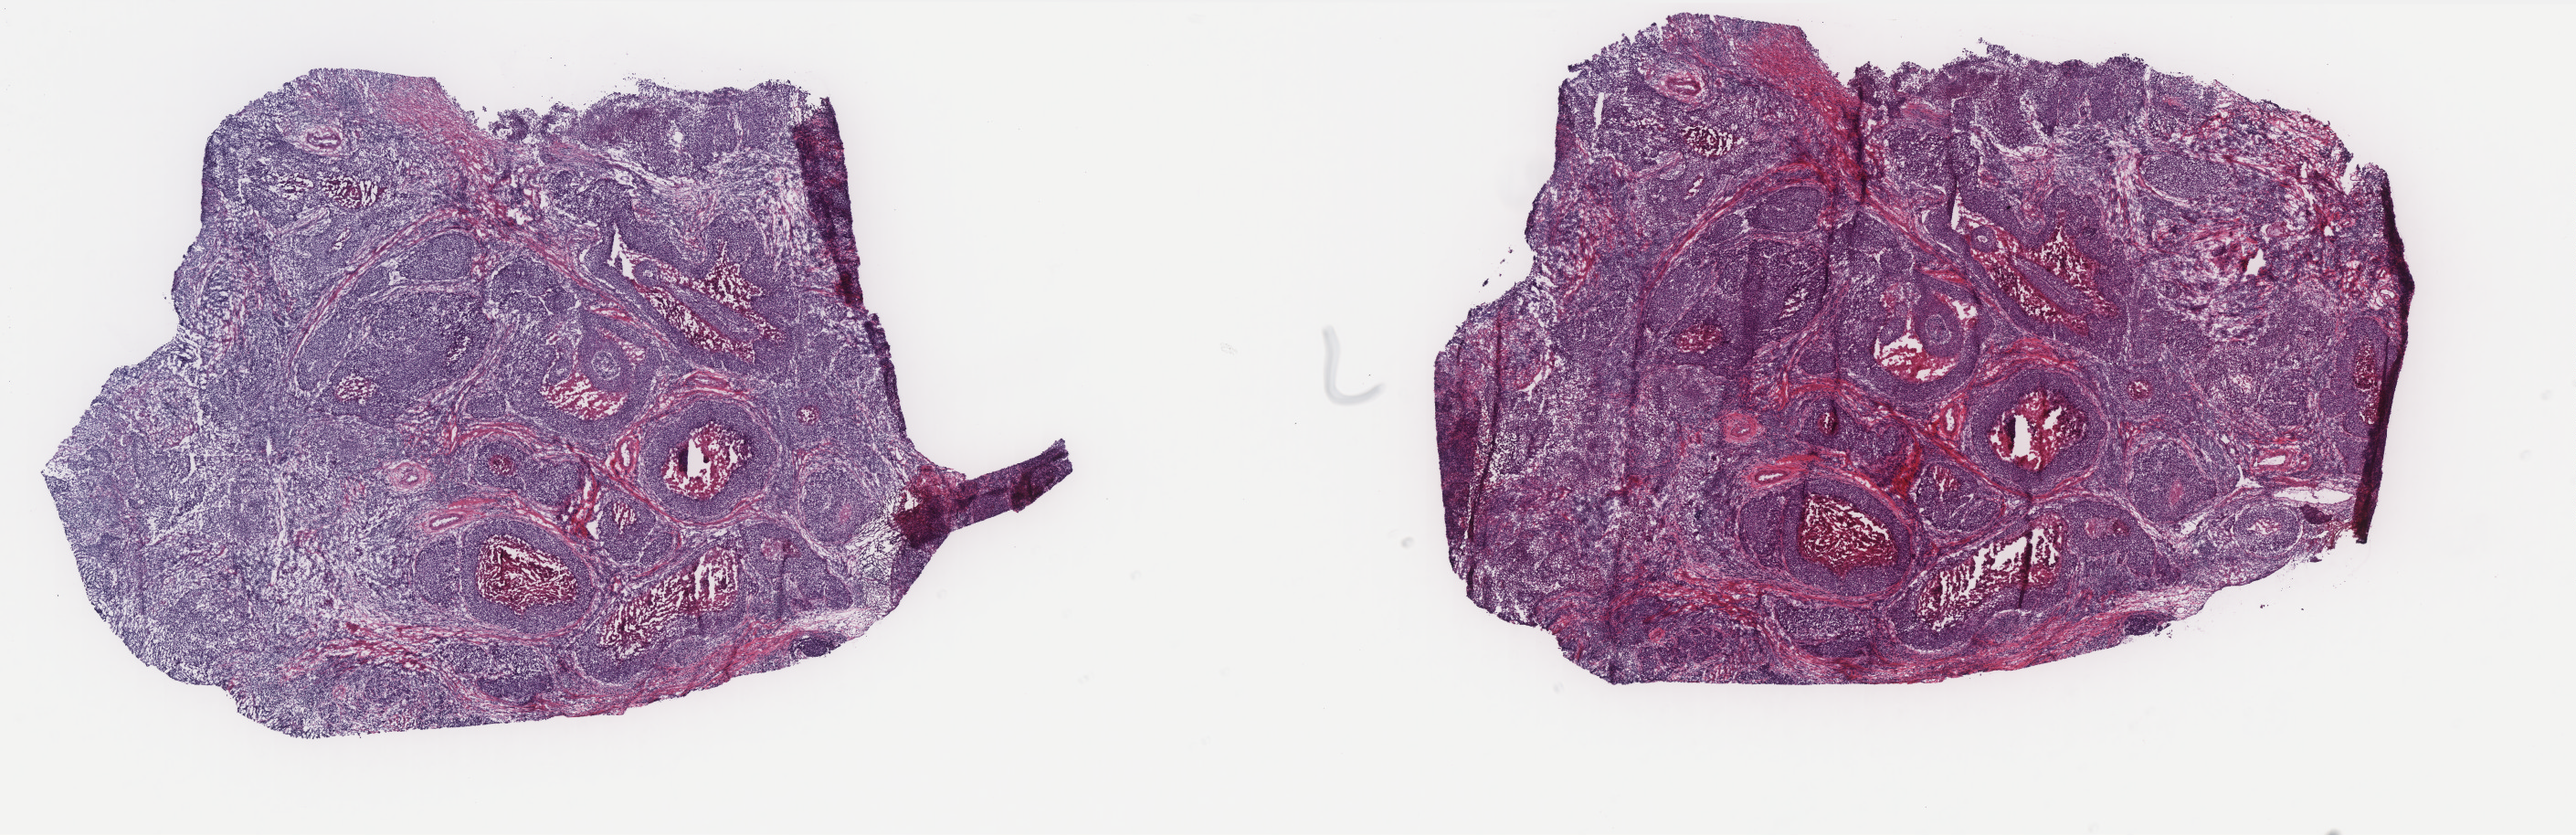
Digitized Hematoxylin and eosin (H&E) stained tissue section (whole slide), a low-resolution overview of the entire scanned area, about 22.6 x 7.3 mm (acquisition: 40x scan), frozen section, sample: primary tumour, cervix. Female, age 53 years at initial diagnosis. Histologic grade: G3 (poorly differentiated). Slide review estimates, as recorded: tumour cells 70%, tumour nuclei 70%, normal cells 0%, stromal cells 20%, necrosis 10%. Inflammatory infiltration, as recorded: lymphocyte infiltration 60%, monocyte infiltration 10%, neutrophil infiltration 20%.
* diagnosis: Squamous cell carcinoma, NOS